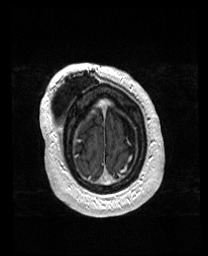
Brain MRI from a brain-tumour surgery series, one axial slice. Position 31 of 176 along the scan axis. T1-weighted post-contrast. 208 × 256 image matrix. Case-level facts recorded for this patient, not image findings: histopathology: Astrocytoma; WHO grade: 4; IDH mutation: yes.
Outlined on this slice (outlined manually by an expert reader):
- previous resection cavity: box from (x=94, y=101) to (x=104, y=111) px